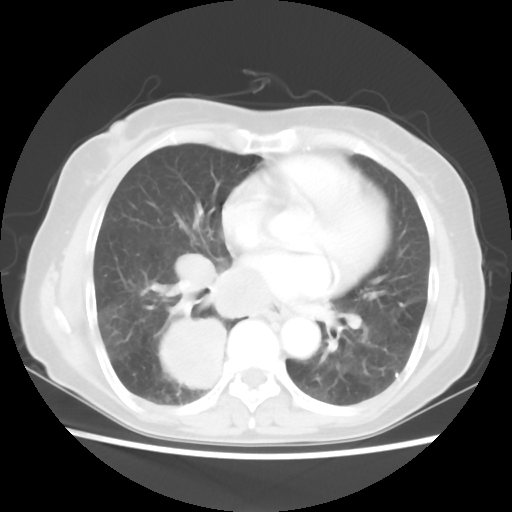
Chest CT, one axial slice; position 27 of 56 along the scan axis; reconstruction kernel STANDARD; 120 kVp; lung window (W 1500 / L -600 HU); 5 mm slice thickness; 512 × 512 image matrix. Female patient, age 66 years. Case-level facts recorded for this patient, not image findings: clinical TNM (as recorded): T2 N3 M0; histopathological grade: G3.
Annotated regions visible in this slice (rectangle marked by the reading radiologist):
- lung tumour (recorded histology: small cell carcinoma): bounding box [x1, y1, x2, y2] px = [156, 313, 230, 392]